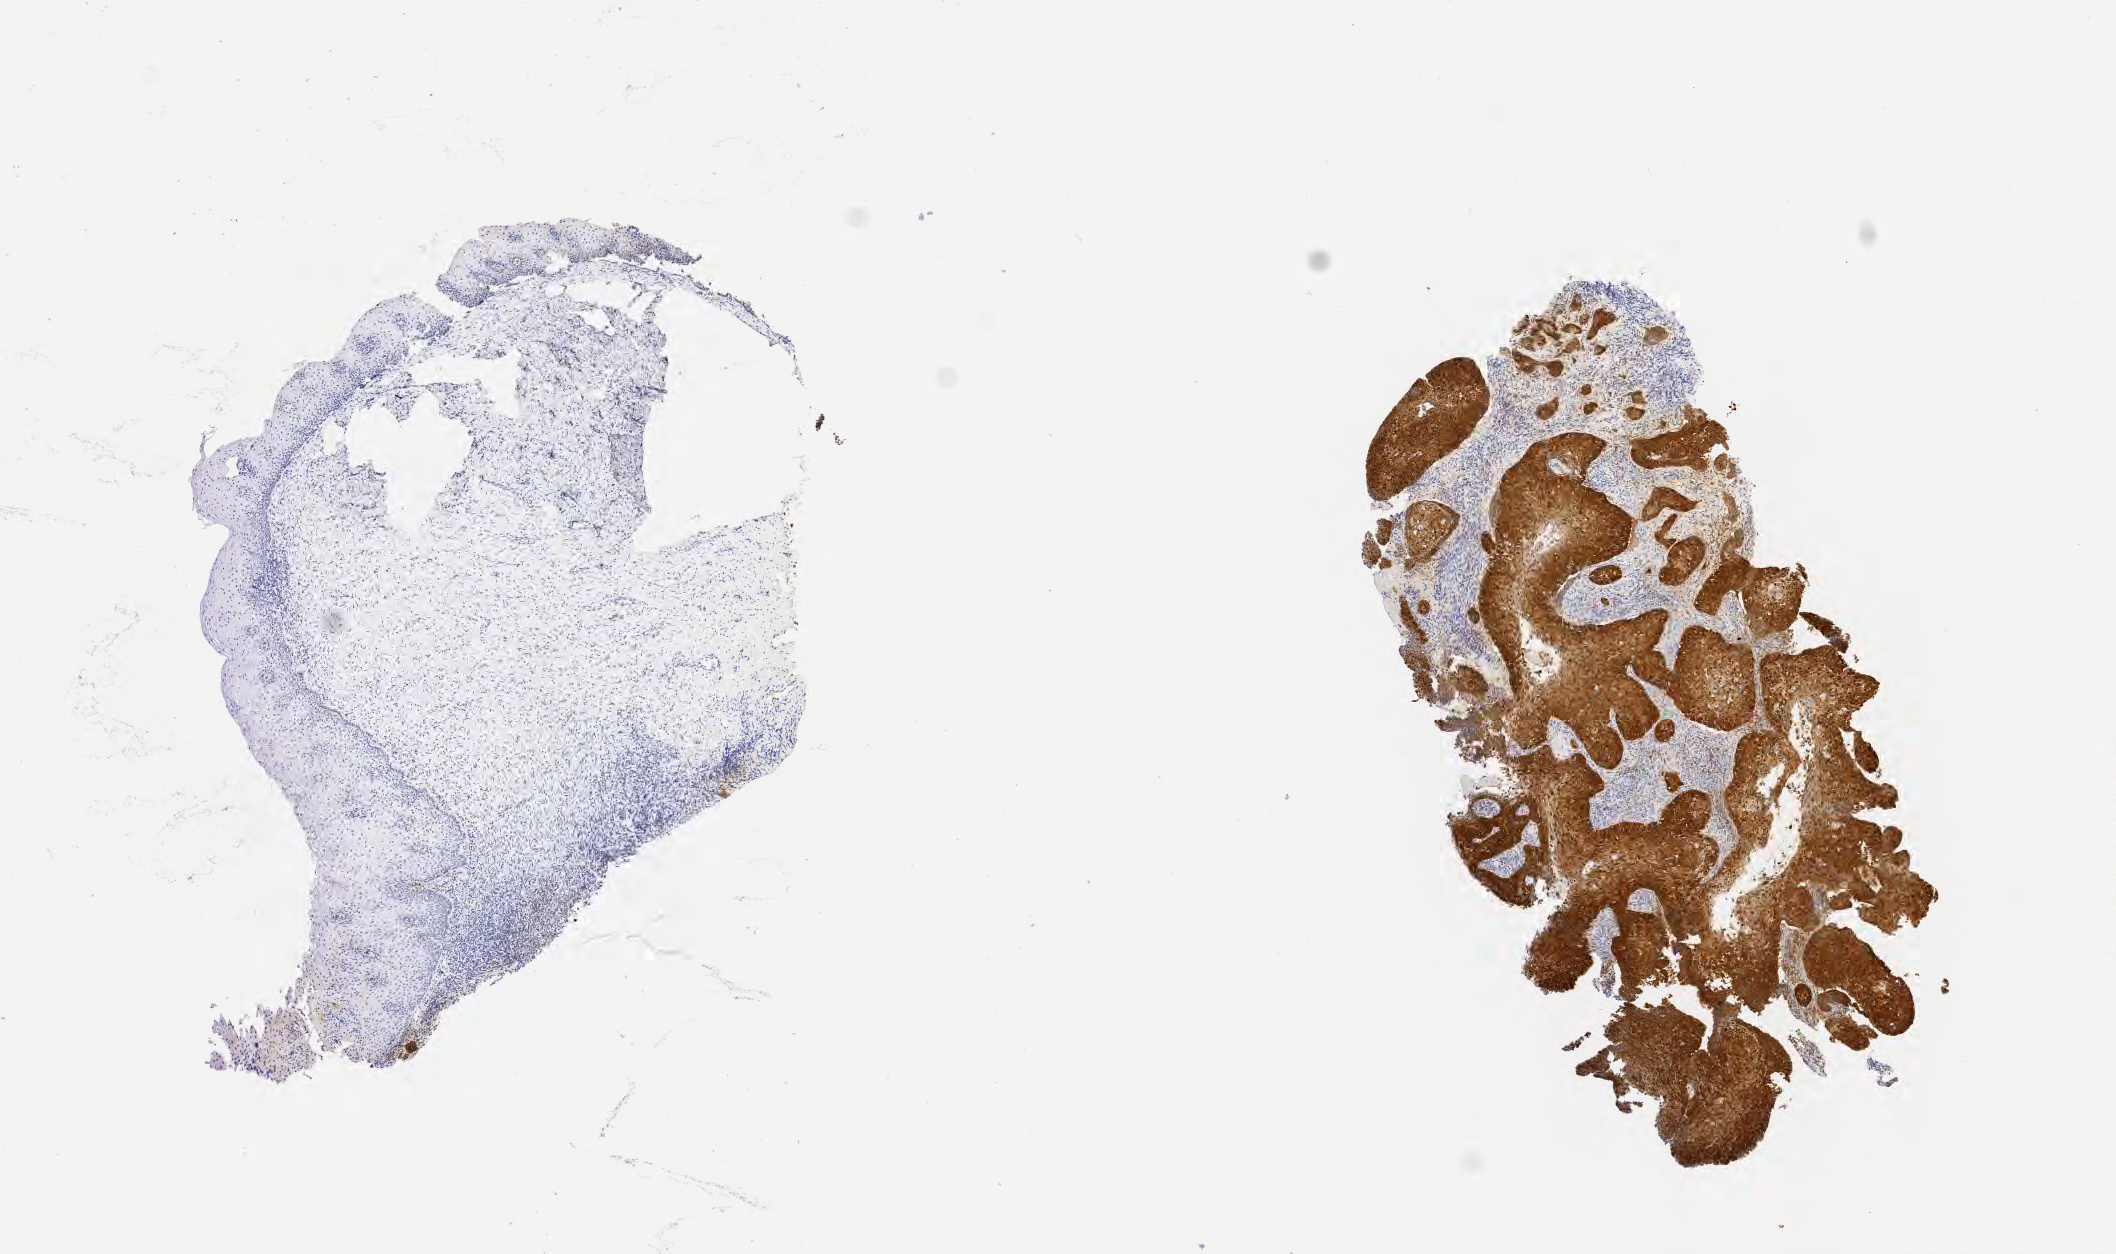
Whole-slide image, immunohistochemical stain for p16 (p16INK4a), a low-resolution overview of the entire scanned area, about 8.6 x 5.1 mm, tumor tissue, site: cervix. Patient: female, age 40 years.
* histologic diagnosis: Squamous cell carcinoma, large cell, nonkeratinizing, NOS